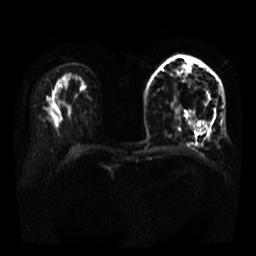
Breast MRI, one axial slice. Slice 21 of 35 in the series (ordered by position). Diffusion-weighted series; image 2 of 4 stored at this slice position (different b-values; order by instance number). 3 T. 5 mm slice thickness. 256 × 256 image matrix, field of view 320 × 320 mm. Female patient.
Structures marked on this image (manually delineated by an expert):
- tumour on diffusion-weighted imaging: box from (x=191, y=111) to (x=206, y=133) px